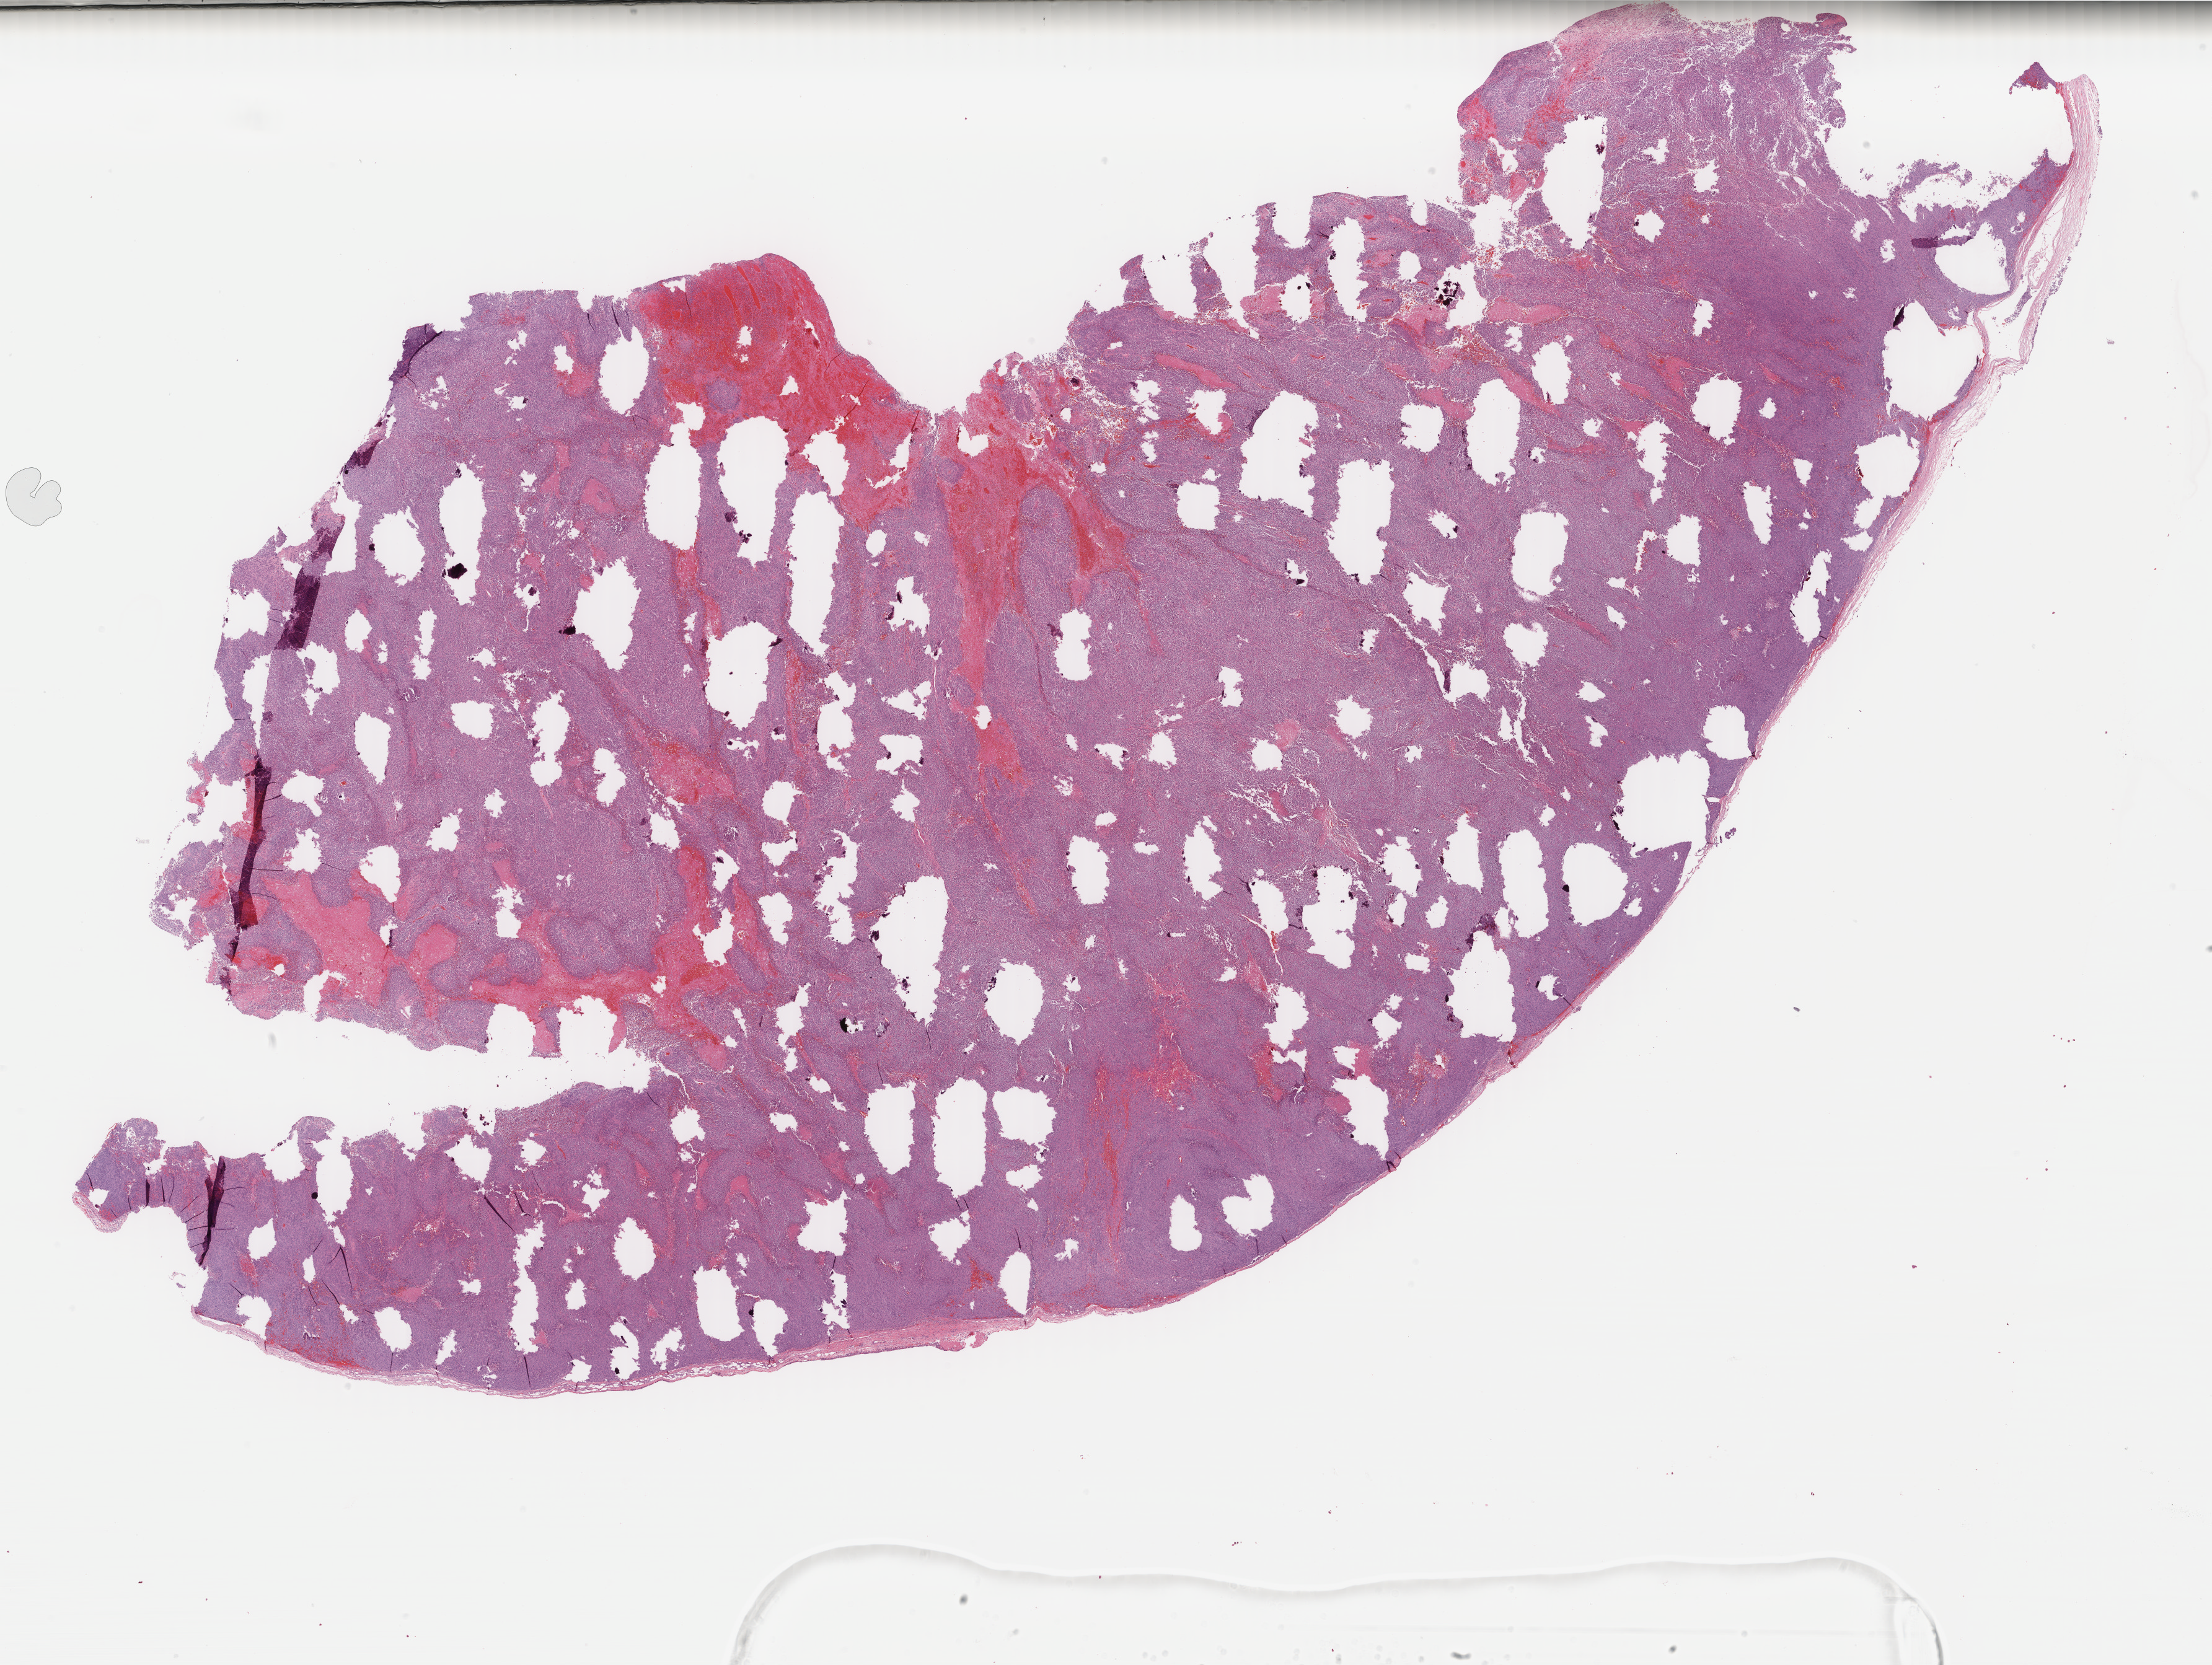
Digitized Hematoxylin and eosin (H&E) stained tissue section (whole slide), low-resolution overview of the scanned area, about 28.3 x 21.3 mm. Formalin-fixed paraffin-embedded (FFPE) diagnostic section. Primary tumour sample from the skin. Male patient; age at initial diagnosis 82 years.
Diagnosis: Malignant melanoma, NOS.